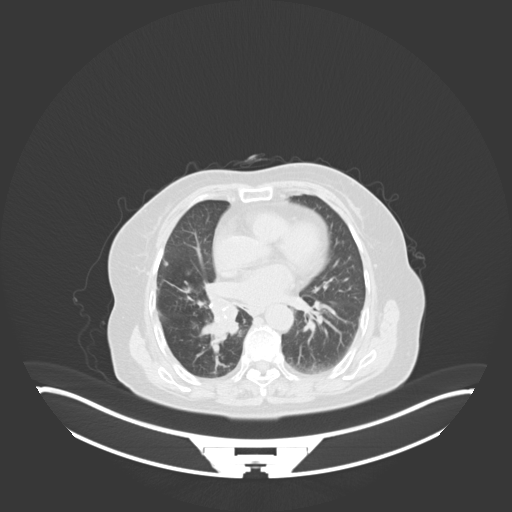
Chest CT, one axial slice; slice 25 of 76 in the series (ordered by position); reconstruction kernel B30f; 120 kVp; lung window (W 1500 / L -600 HU); 3 mm slice thickness; 512 × 512 image matrix, field of view 500 × 500 mm. Female patient, age 75 years. Case-level facts recorded for this patient, not image findings: clinical TNM (as recorded): T1b N0 M1a; histopathological grade: G1.
Annotated regions visible in this slice (bounding box drawn by a radiologist):
- lung tumour (recorded histology: squamous cell carcinoma): bounding box <199,296,238,351> (left, top, right, bottom; pixels)